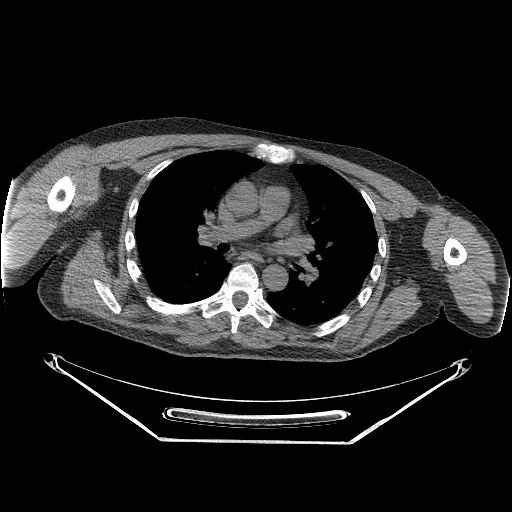
CT of an extremity soft-tissue mass (from a PET/CT study), one axial slice; slice 176 of 267 in the series (ordered by position); soft-tissue window (W 400 / L 40 HU); 3.75 mm slice thickness; 512 × 512 image matrix, field of view 500 × 500 mm. Male patient. From the clinical record (not read from this slice): histological type: pleiomorphic spindle cell undifferentiated; grade: high; site of the primary tumour: right parascapusular.
Annotated regions visible in this slice (expert contour drawn on MRI and transferred to this co-registered scan by the dataset authors):
- gross tumour volume including surrounding oedema: bounding box (x1, y1, x2, y2) in pixels: (157, 308, 227, 332)